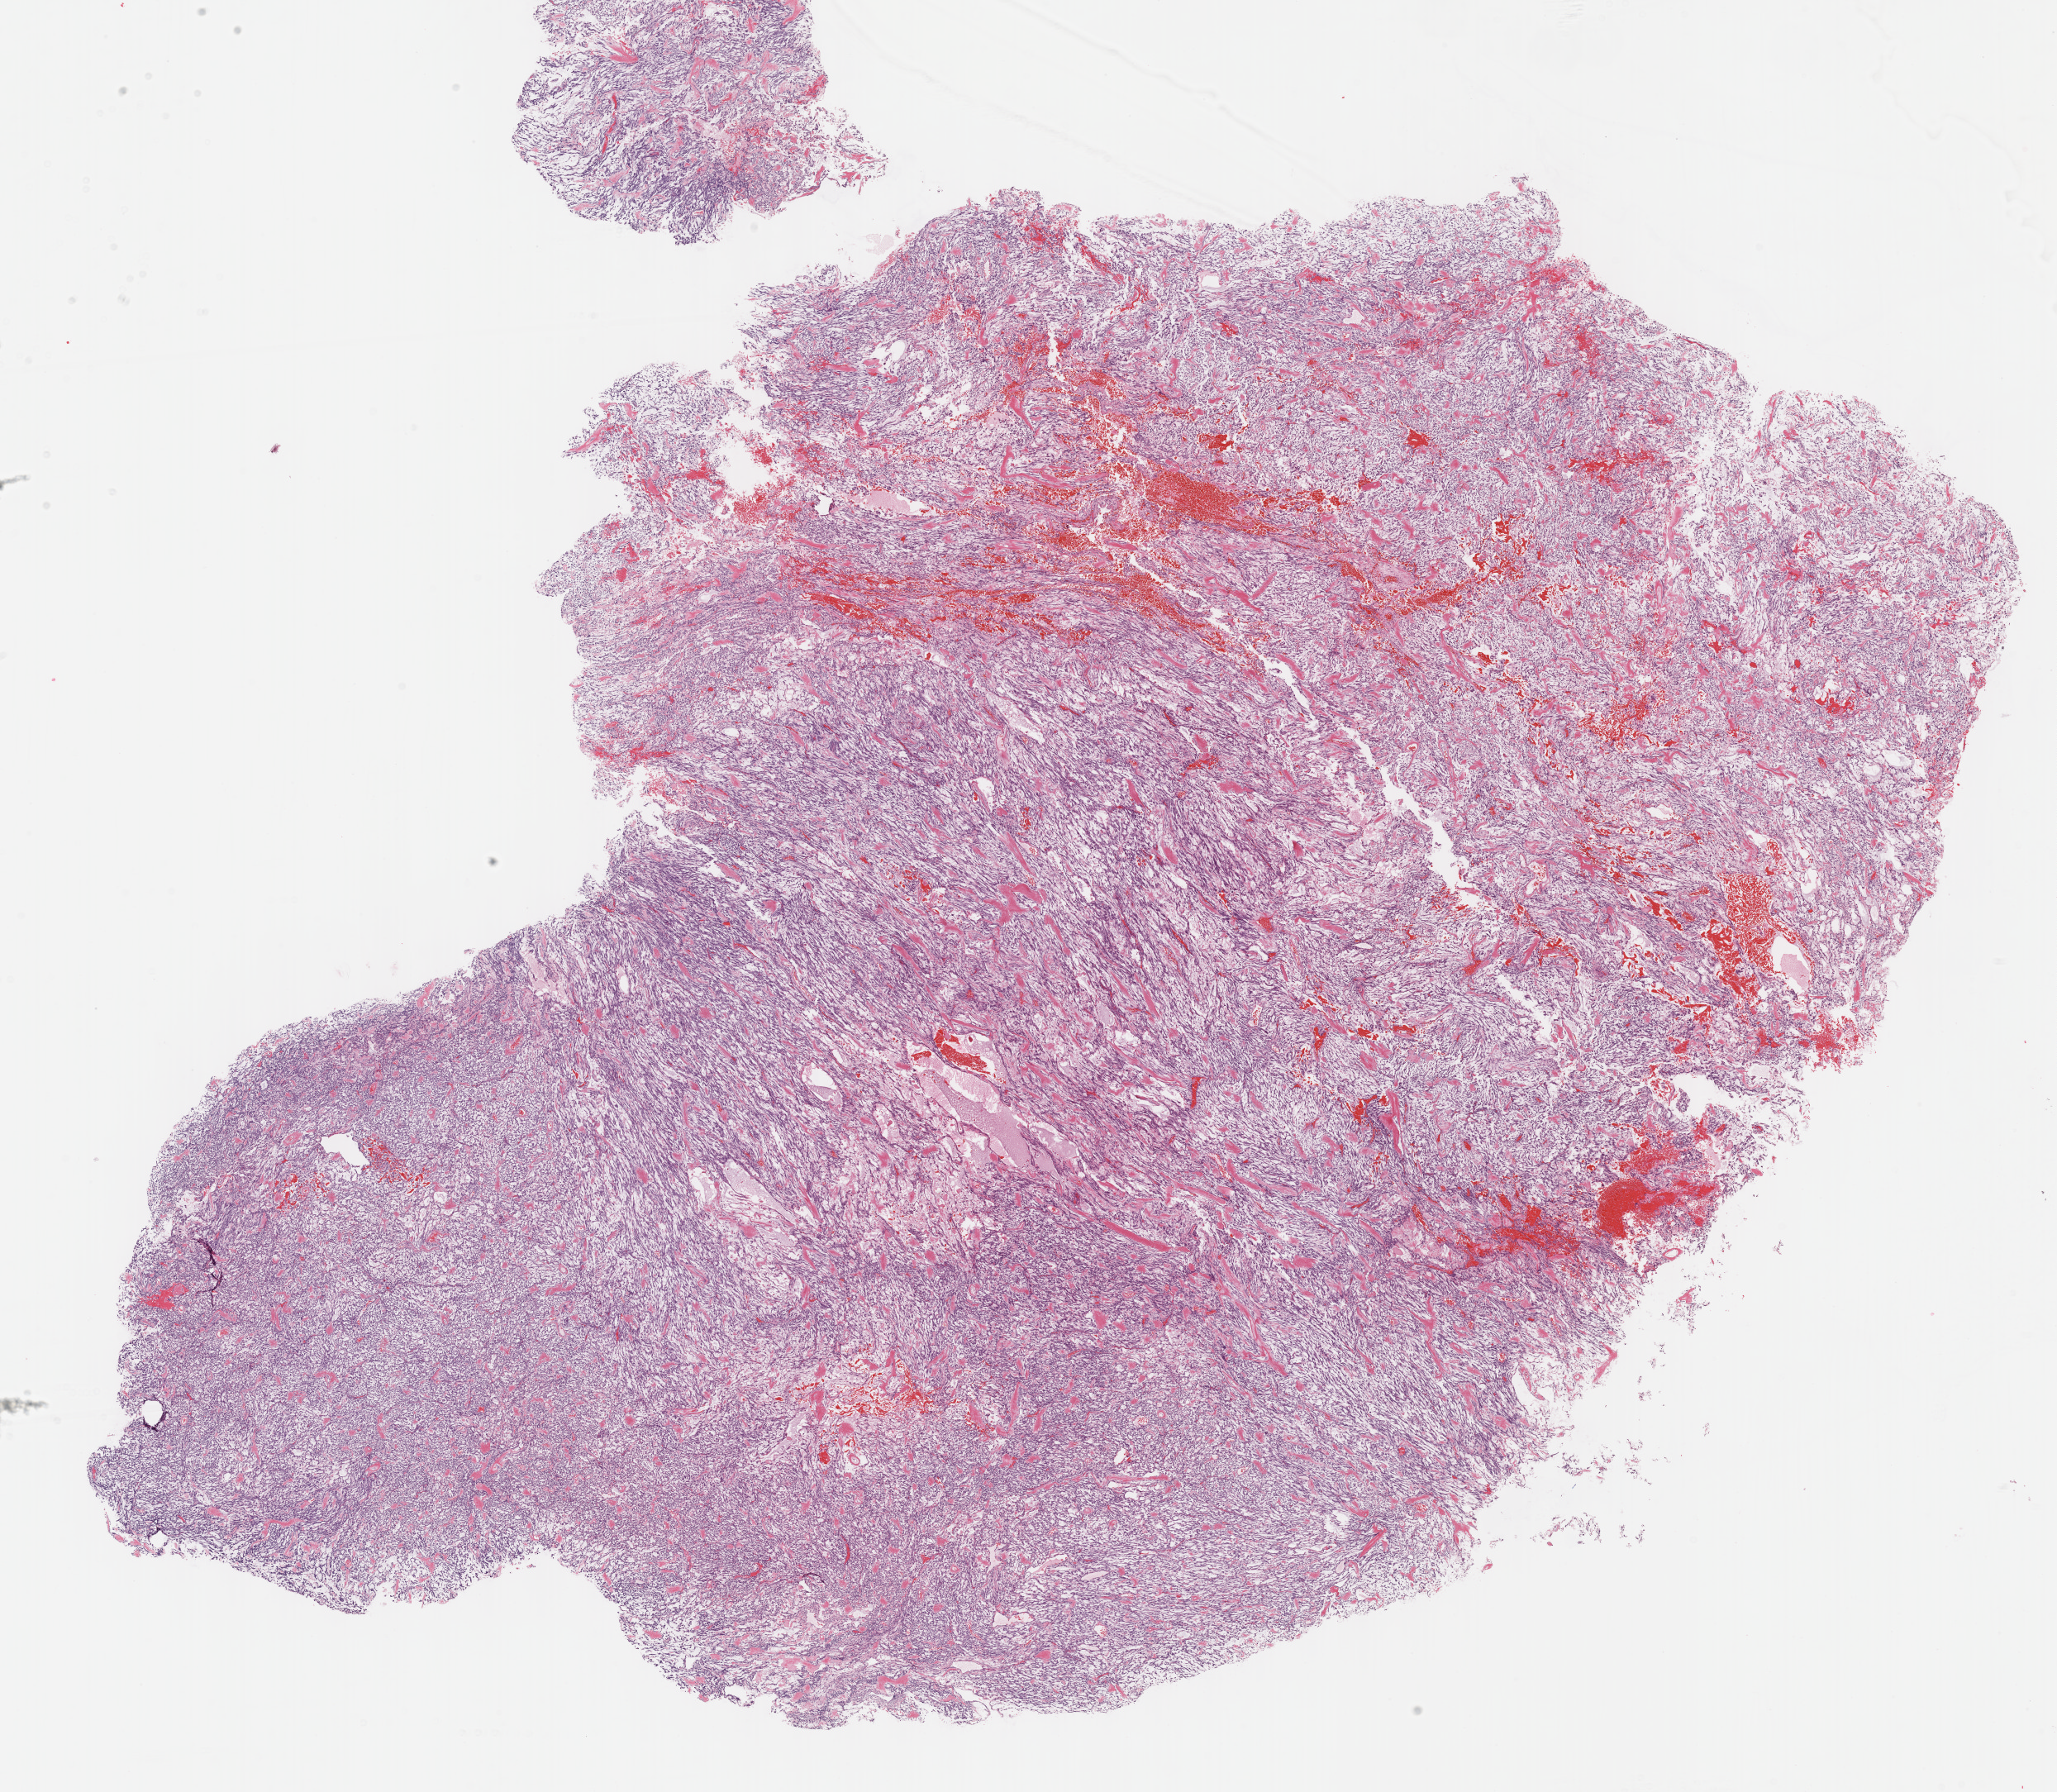
Digitized Hematoxylin and eosin (H&E) stained tissue section (whole slide), whole scanned area (about 20.1 x 17.5 mm, from a 40x scan) shown as a low-resolution overview, formalin-fixed paraffin-embedded (FFPE) diagnostic section, primary tumour sample from the corpus uteri. Female, age 57 years at initial diagnosis.
Pathologic diagnosis: Myxoid leiomyosarcoma (isthmus uteri).